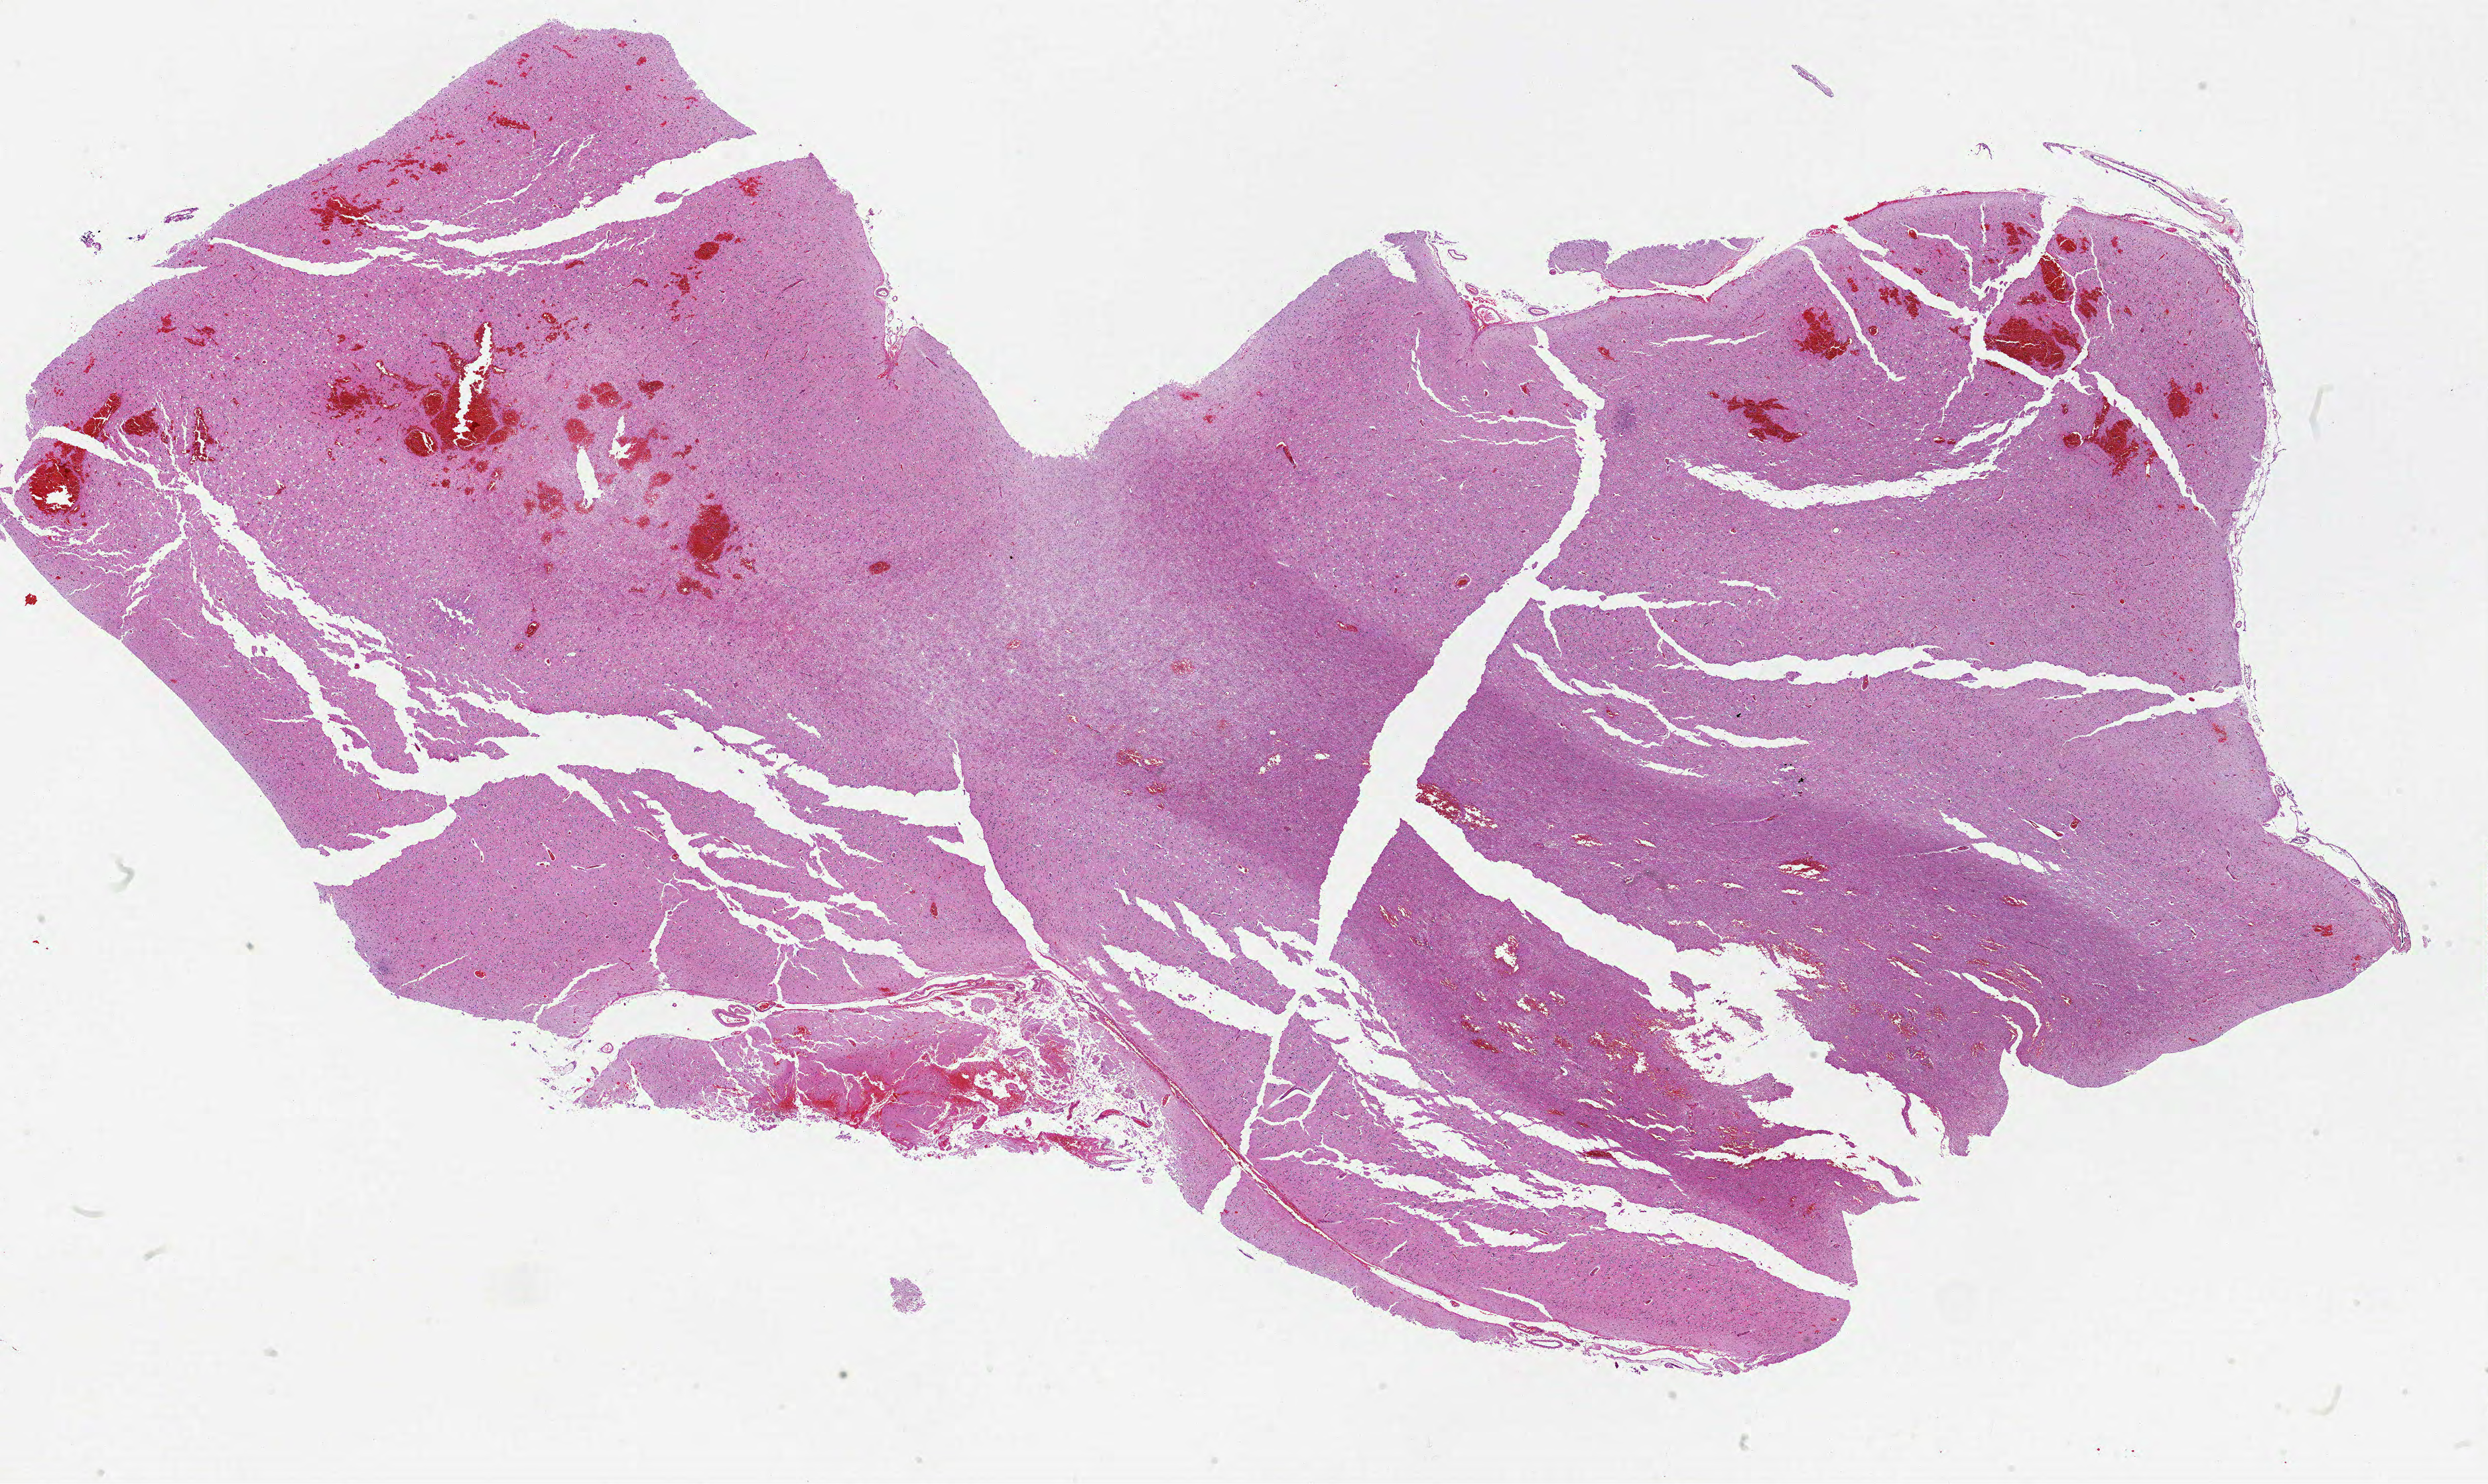
H&E-stained whole-slide image, low-resolution overview of the scanned area, about 30.0 x 17.9 mm, formalin-fixed paraffin-embedded (FFPE) diagnostic section, primary tumour sample from the brain. Male patient; age at initial diagnosis 55 years.
* histologic diagnosis: Glioblastoma